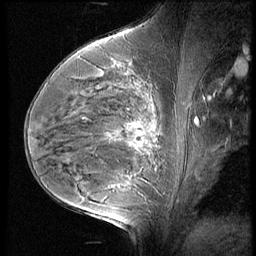
Breast MRI (dynamic contrast-enhanced), one sagittal slice. Slice 35 of 60 in the series (ordered by position). 3 images stored at this slice position (order not interpretable as contrast timing). 1.5 T. TE 4.2 ms, TR 9 ms. 2.5 mm slice thickness. 256 × 256 image matrix. Patient: female, 35 years. Case-level facts recorded for this patient, not image findings: setting: breast cancer imaged before/during neoadjuvant chemotherapy; receptor status: HR-positive, HER2-negative.
Annotated regions visible in this slice (semi-automatic segmentation, software-assisted and operator-edited):
- analysis volume of interest (the breast-tissue region the enhancement analysis was run in; not a lesion): bounding box <56,58,176,202> (left, top, right, bottom; pixels)
- tumour enhancement mask (voxels above the 140 % enhancement threshold inside the analysis volume of interest): <119,140,156,190>